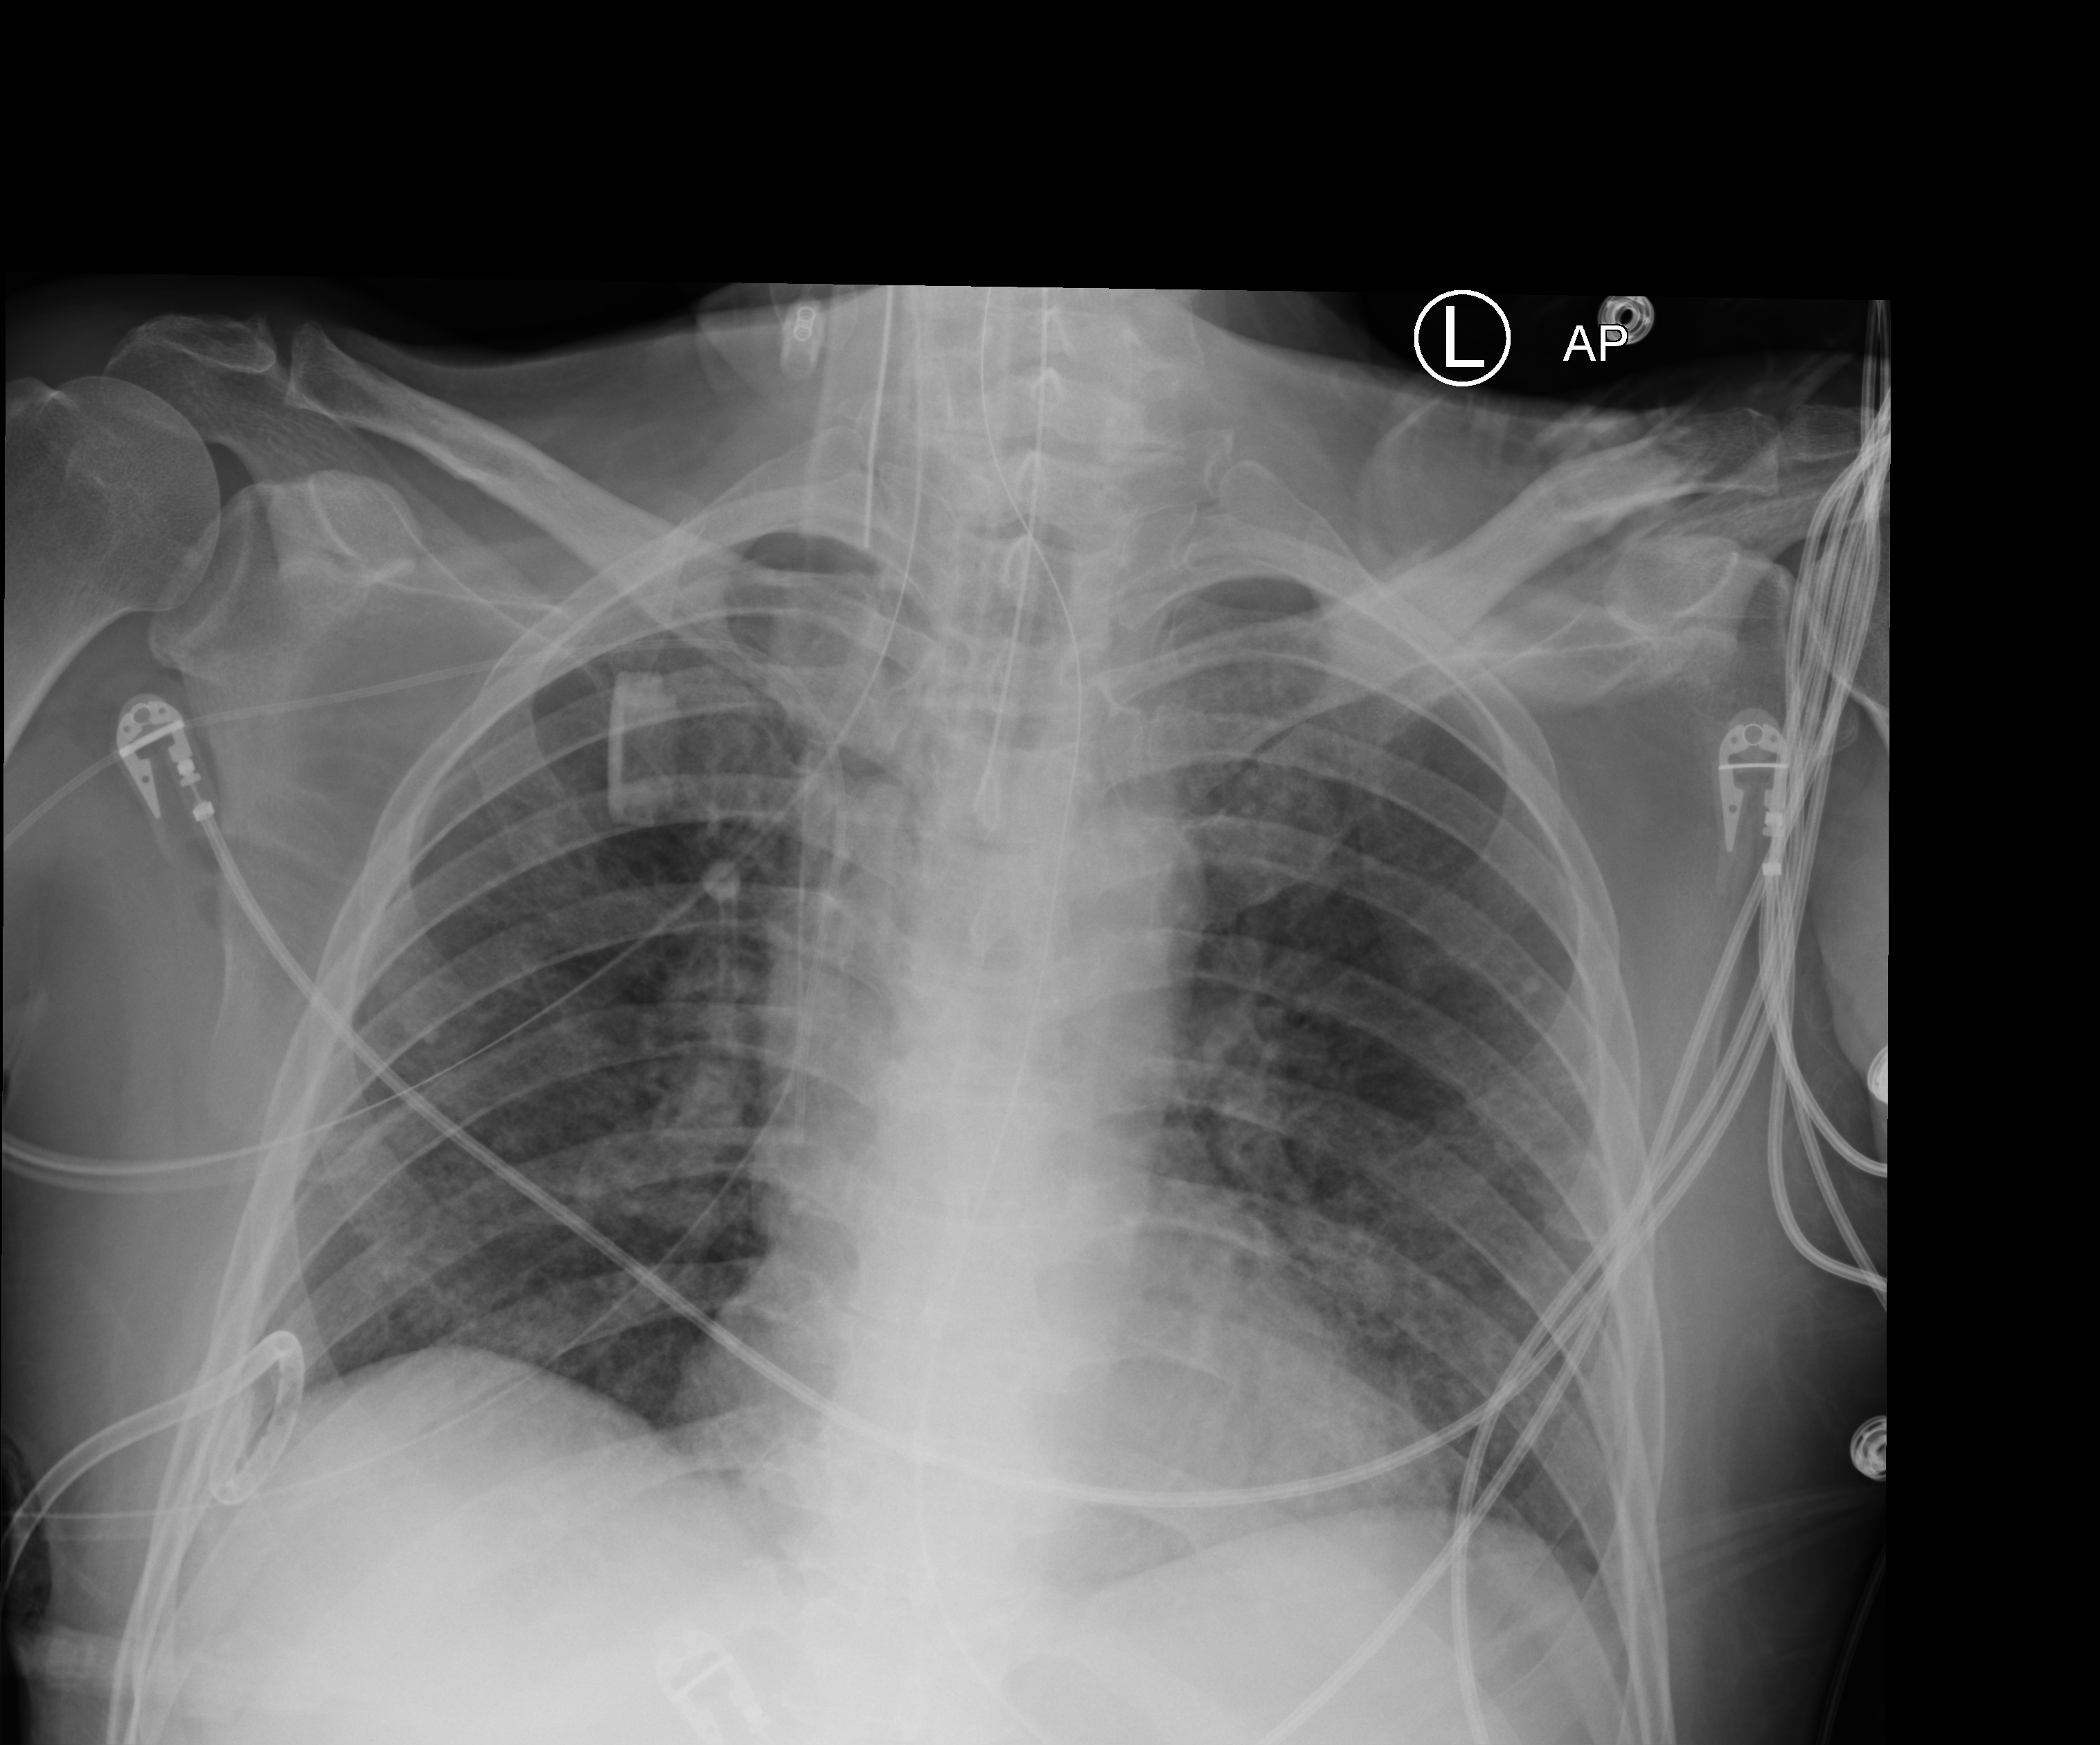
Bedside chest radiograph (computed radiography); anteroposterior (AP) projection. Male patient hospitalised with COVID-19, age 18–59 years.
Admission-level facts for this patient (not findings on this image; timing relative to this image not recorded): admitted to intensive care during this hospital stay: yes.